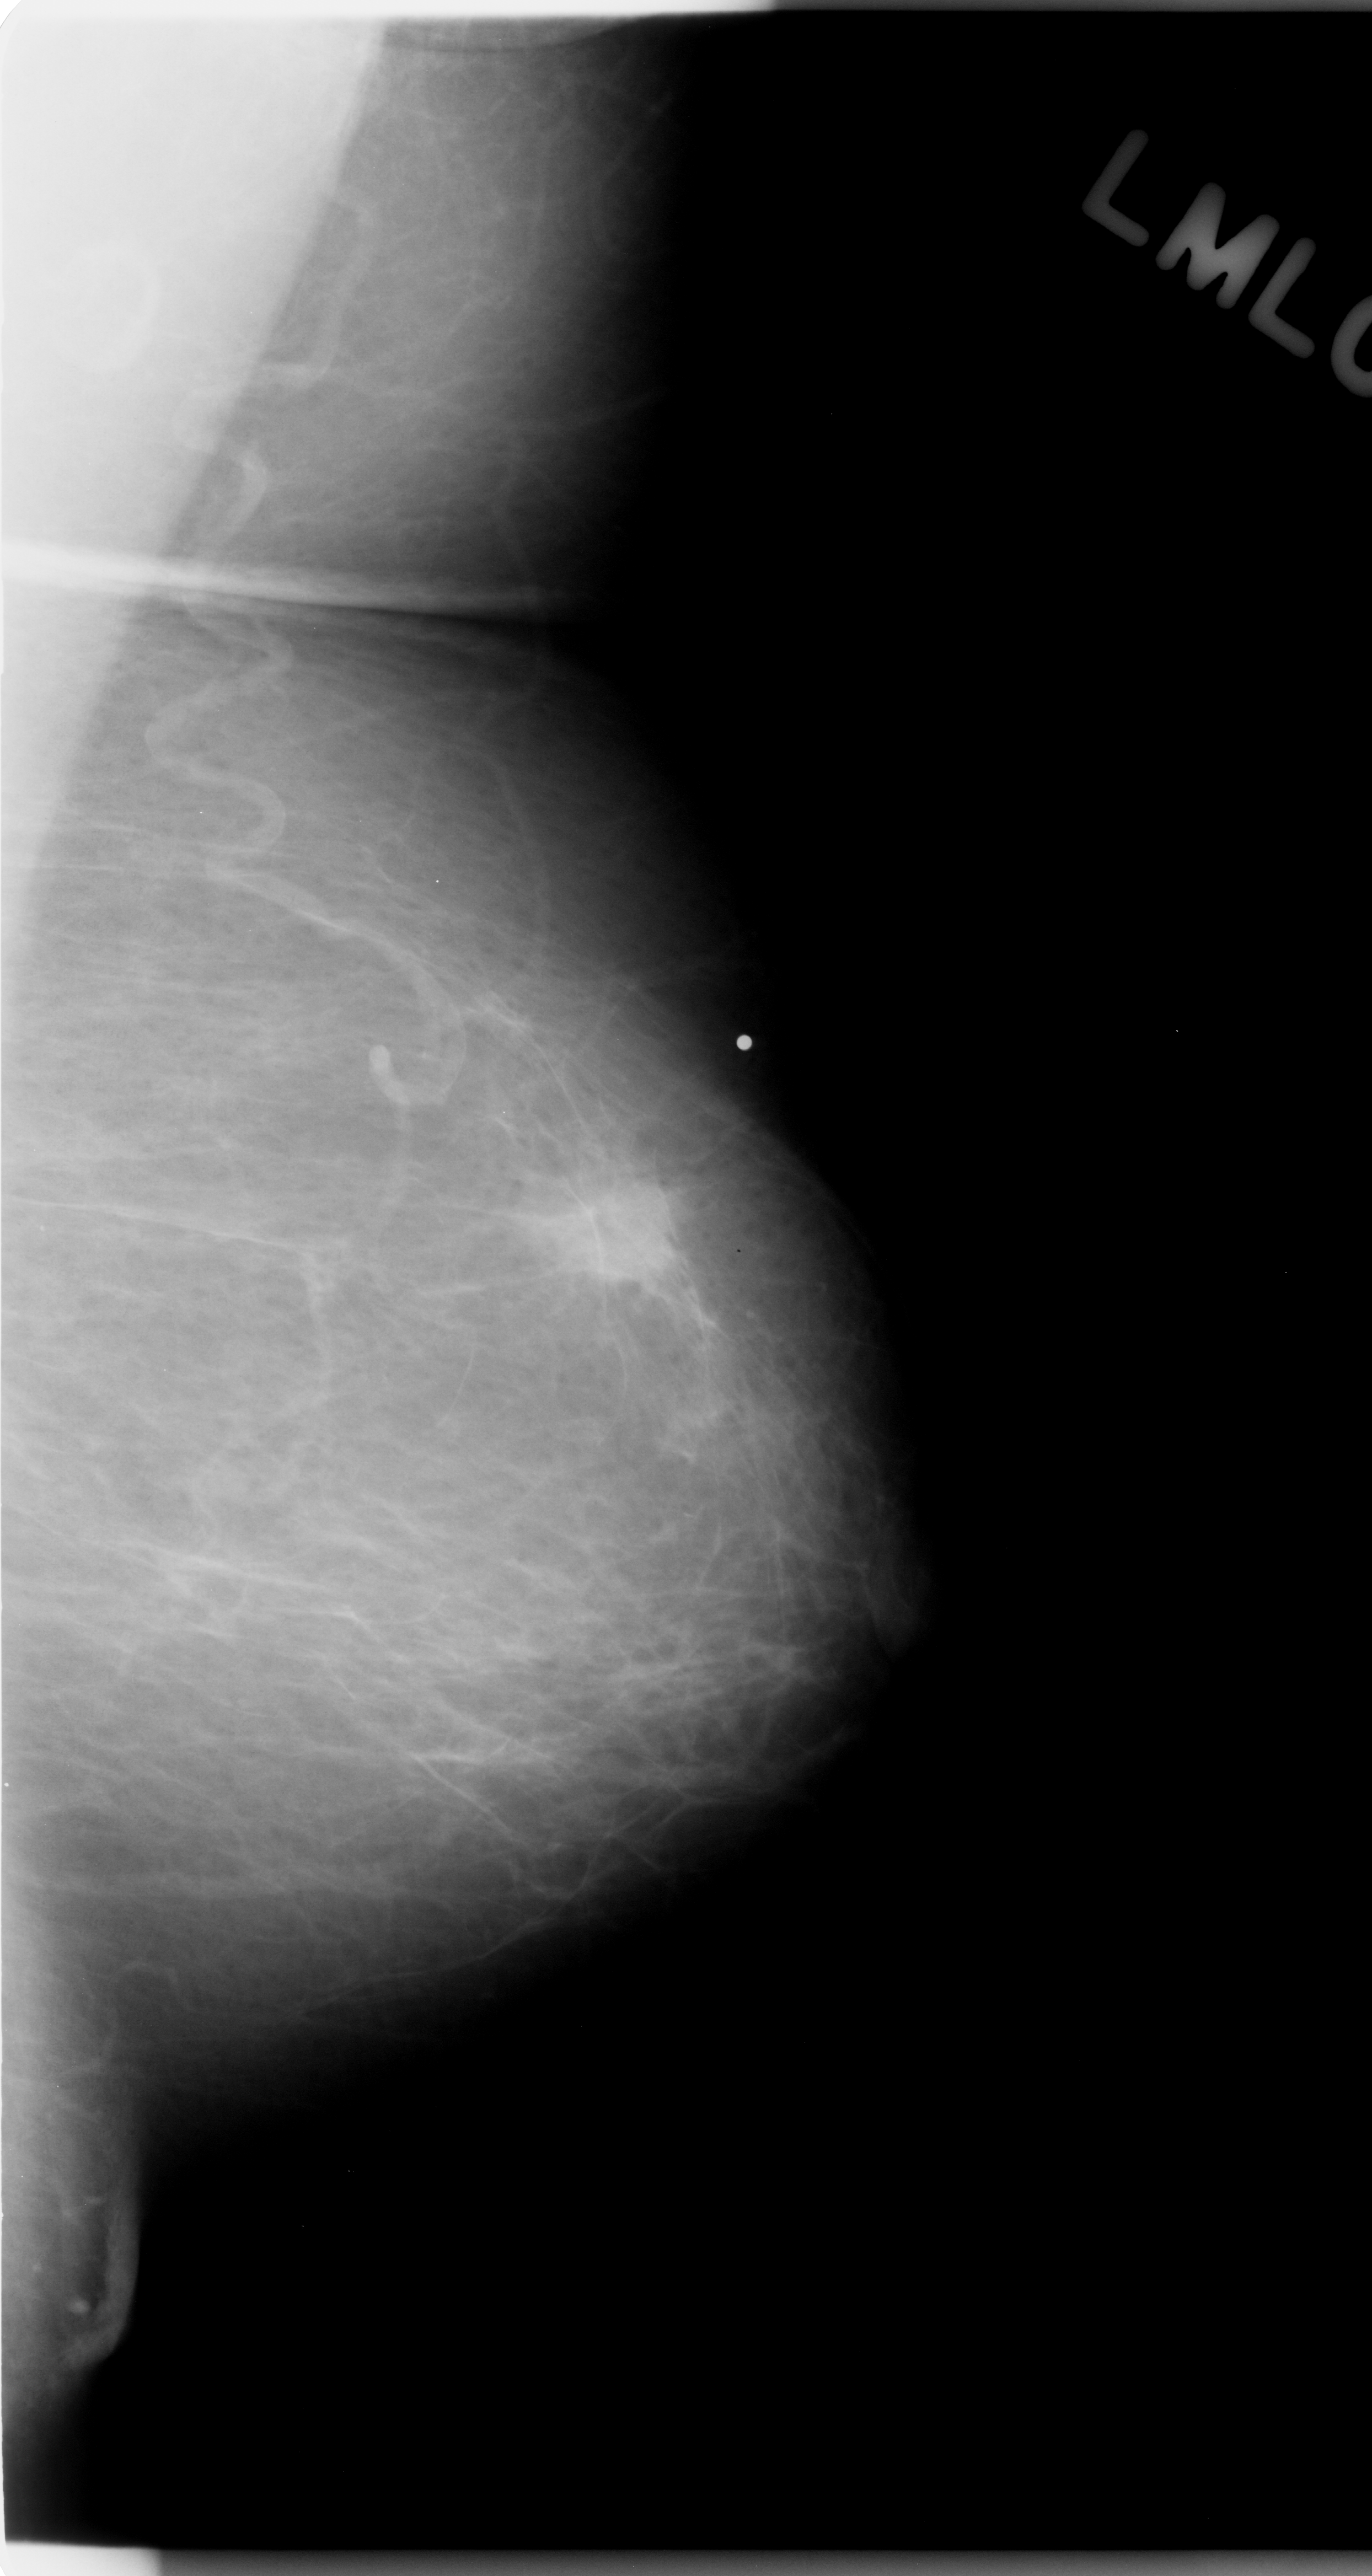
Mammogram (digitized film); left breast; mediolateral oblique (MLO) view.
Abnormality record for this image: mass, shape irregular, margins ill defined; BI-RADS assessment category 5; subtlety rating 5 on a 1 (subtle) to 5 (obvious) scale; pathology result (as recorded, not read from the image): malignant.